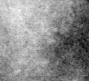
Region of interest cut from a scanned film mammogram (one marked finding); right breast; MLO view.
Finding: calcifications, morphology pleomorphic, distribution clustered; BI-RADS assessment category 4; subtlety rating 3 on a 1 (subtle) to 5 (obvious) scale; pathology result (as recorded, not read from the image): malignant.